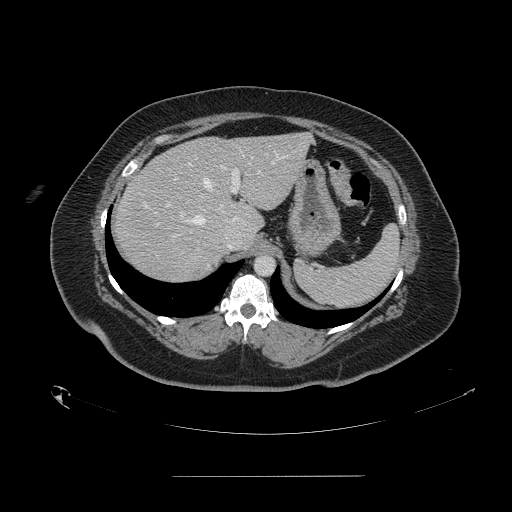
Contrast-enhanced abdominal CT, one axial slice. Position 112 of 164 along the scan axis. 120 kVp. Soft-tissue window (W 400 / L 40 HU). 2.5 mm slice thickness. 512 × 512 image matrix, field of view 495 × 495 mm. Female patient, age 52 years. From the clinical record (not read from this slice): diagnosis: colorectal cancer liver metastases, imaged before liver resection; multiple liver metastases: yes; largest metastasis: 3.5 cm; disease in both lobes: no.
Annotated regions visible in this slice (outlined manually by an expert reader):
- hepatic veins: bounding box (x1, y1, x2, y2) in pixels: (153, 154, 287, 233)
- liver: (113, 134, 311, 283)
- planned liver remnant (the part of the liver to remain after resection): (171, 134, 311, 228)
- portal vein (with intrahepatic branches): (167, 163, 250, 215)